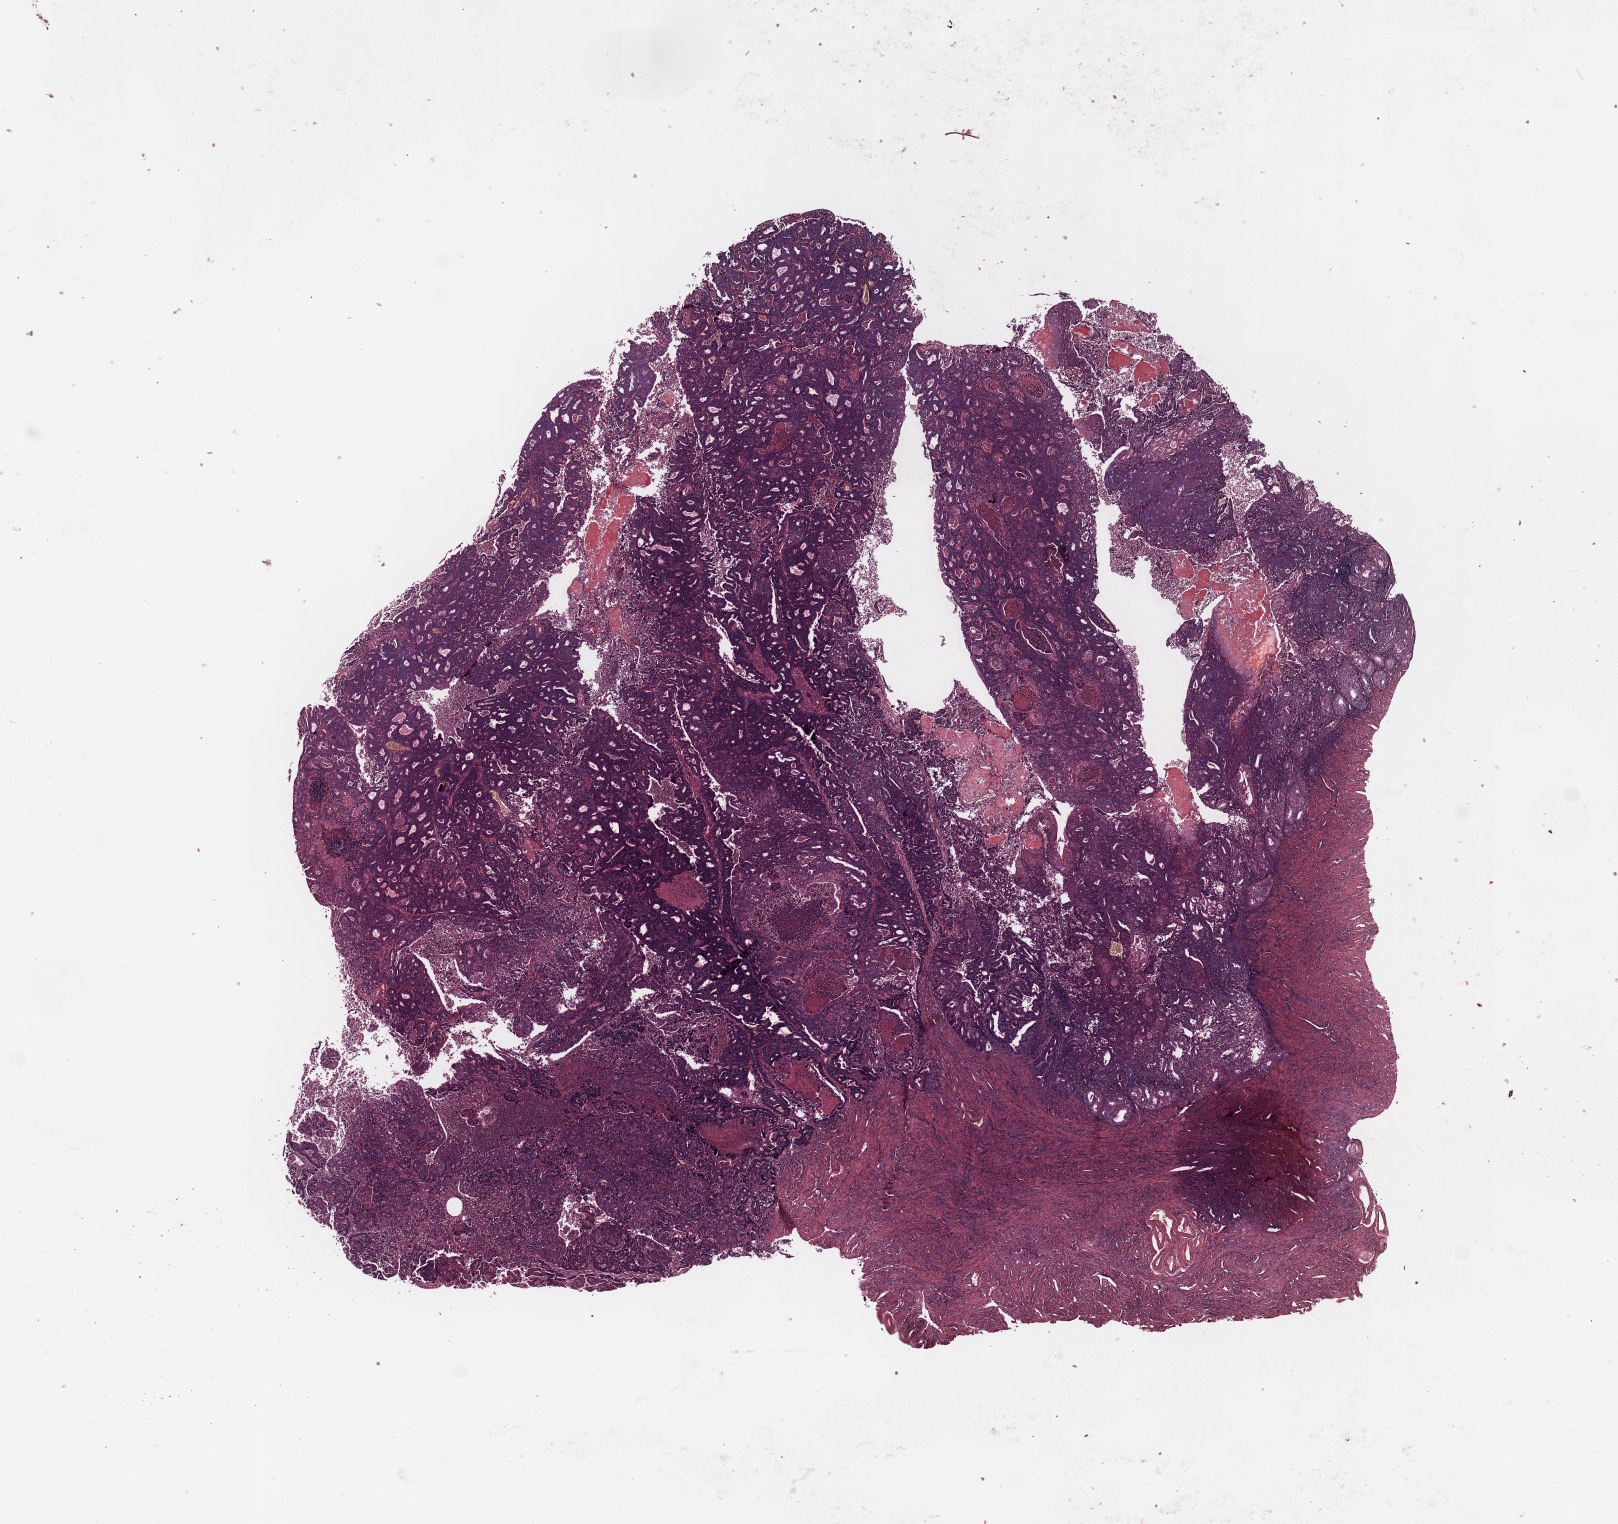
Digitized H&E-stained tissue section (whole slide), shown as a low-resolution overview of the whole scanned area (about 12.8 x 12.1 mm, from a 20x scan). Uterus, tumour tissue. Patient: female, age 77 years. Histologic grade: G2 (moderately differentiated).
Histologic diagnosis: Endometrioid adenocarcinoma, NOS. AJCC pathologic stage: I.